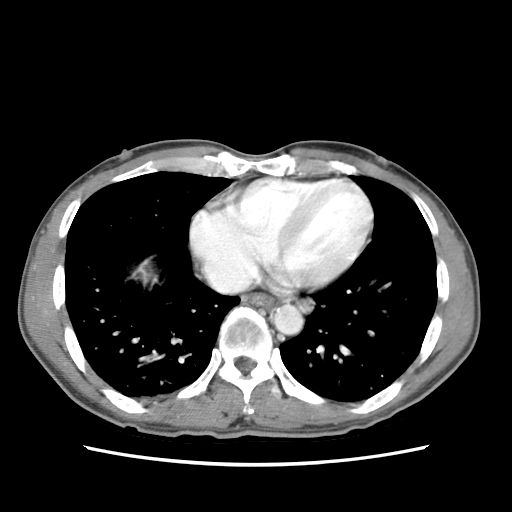
Contrast-enhanced abdominal CT (liver protocol), one axial slice. Position 74 of 79 along the scan axis. 120 kVp. Soft-tissue window (W 400 / L 40 HU). 512 × 512 image matrix, field of view 320 × 320 mm. From the clinical record (not read from this slice): diagnosis: hepatocellular carcinoma (patient treated with transarterial chemoembolisation; whether this scan precedes or follows treatment is not stated here); TNM stage (as recorded): Stage-IIIB; Child-Pugh class: A; tumour differentiation: moderately differentiated; tumour nodularity: multinodular.
Outlined on this slice (semi-automatic segmentation, software-assisted and operator-edited):
- liver parenchyma outside the tumour (the mass and vessels are separate outlines, so this box may not span the whole liver): box from (x=132, y=256) to (x=156, y=282) px